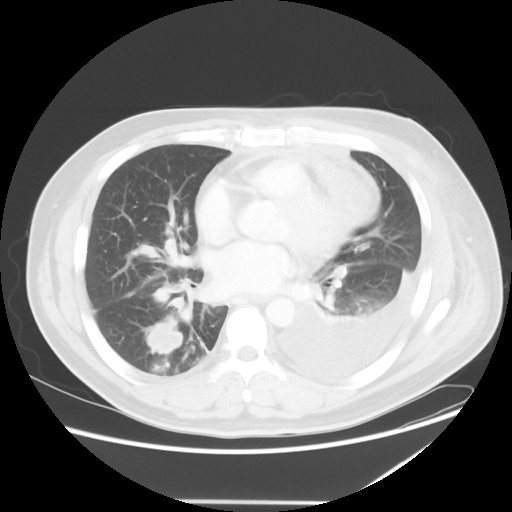
Chest CT, one axial slice; slice 24 of 52 in the series (ordered by position); reconstruction kernel STANDARD; 120 kVp; lung window (W 1500 / L -600 HU); 5 mm slice thickness; 512 × 512 image matrix. Male patient, age 42 years. From the clinical record (not read from this slice): clinical TNM (as recorded): T2 N1 M1.
Outlined on this slice (bounding box drawn by a radiologist):
- lung tumour (recorded histology: adenocarcinoma): box from (x=137, y=315) to (x=189, y=362) px